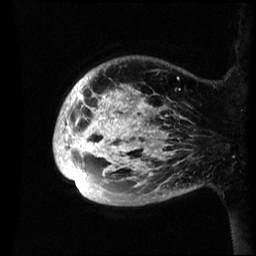
Breast MRI (dynamic contrast-enhanced), one sagittal slice. Slice 8 of 60 in the series (ordered by position). Dynamic contrast-enhanced series, image 2 of 3 at this slice position (ordered by acquisition). 1.5 T. TE 4.2 ms, TR 8.4 ms. 256 × 256 image matrix, field of view 230 × 230 mm. Female patient, age 48 years.
Structures marked on this image (semi-automatic segmentation, software-assisted and operator-edited):
- analysis volume of interest (the breast-tissue region the enhancement analysis was run in; not a lesion): bounding box <53,60,195,206> (left, top, right, bottom; pixels)
- tumour enhancement mask (voxels above the 70 % enhancement threshold inside the analysis volume of interest): <53,80,174,189>